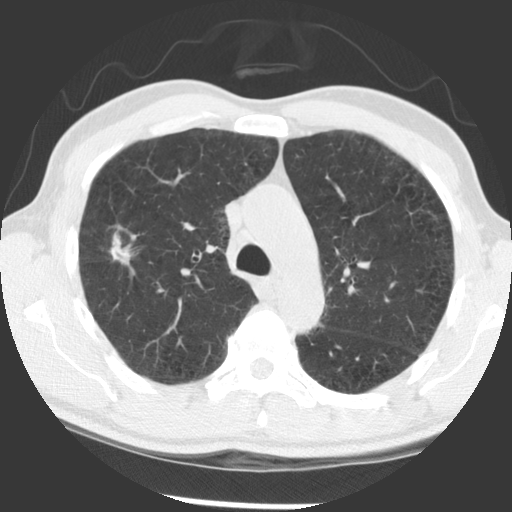
Chest CT (low-dose screening protocol), one axial image. First (baseline) screen. Lung window (W 1500 / L -600 HU). Slice 98 of 140 in the series. Male participant, aged 56 years at enrolment. Current smoker at enrolment.
Lesion marked by an expert reader, bounding box <69,228,138,283> (left, top, right, bottom; pixels). Reader record for this screening exam (exam-level; its link to the box is not recorded): non-calcified nodule or mass ≥4 mm, right upper lobe, 12 × 7 mm, spiculated (stellate) margins, soft tissue attenuation. Official screen result: positive, change unspecified: nodule(s) >= 4 mm or enlarging nodule(s), mass(es), or other non-specific abnormalities suspicious for lung cancer. Later outcome: lung cancer diagnosed 676 days after this screen — squamous cell carcinoma, NOS, right upper lobe, right middle lobe, moderately differentiated (G2), stage IB (AJCC 6th edition), 70 mm at pathology.